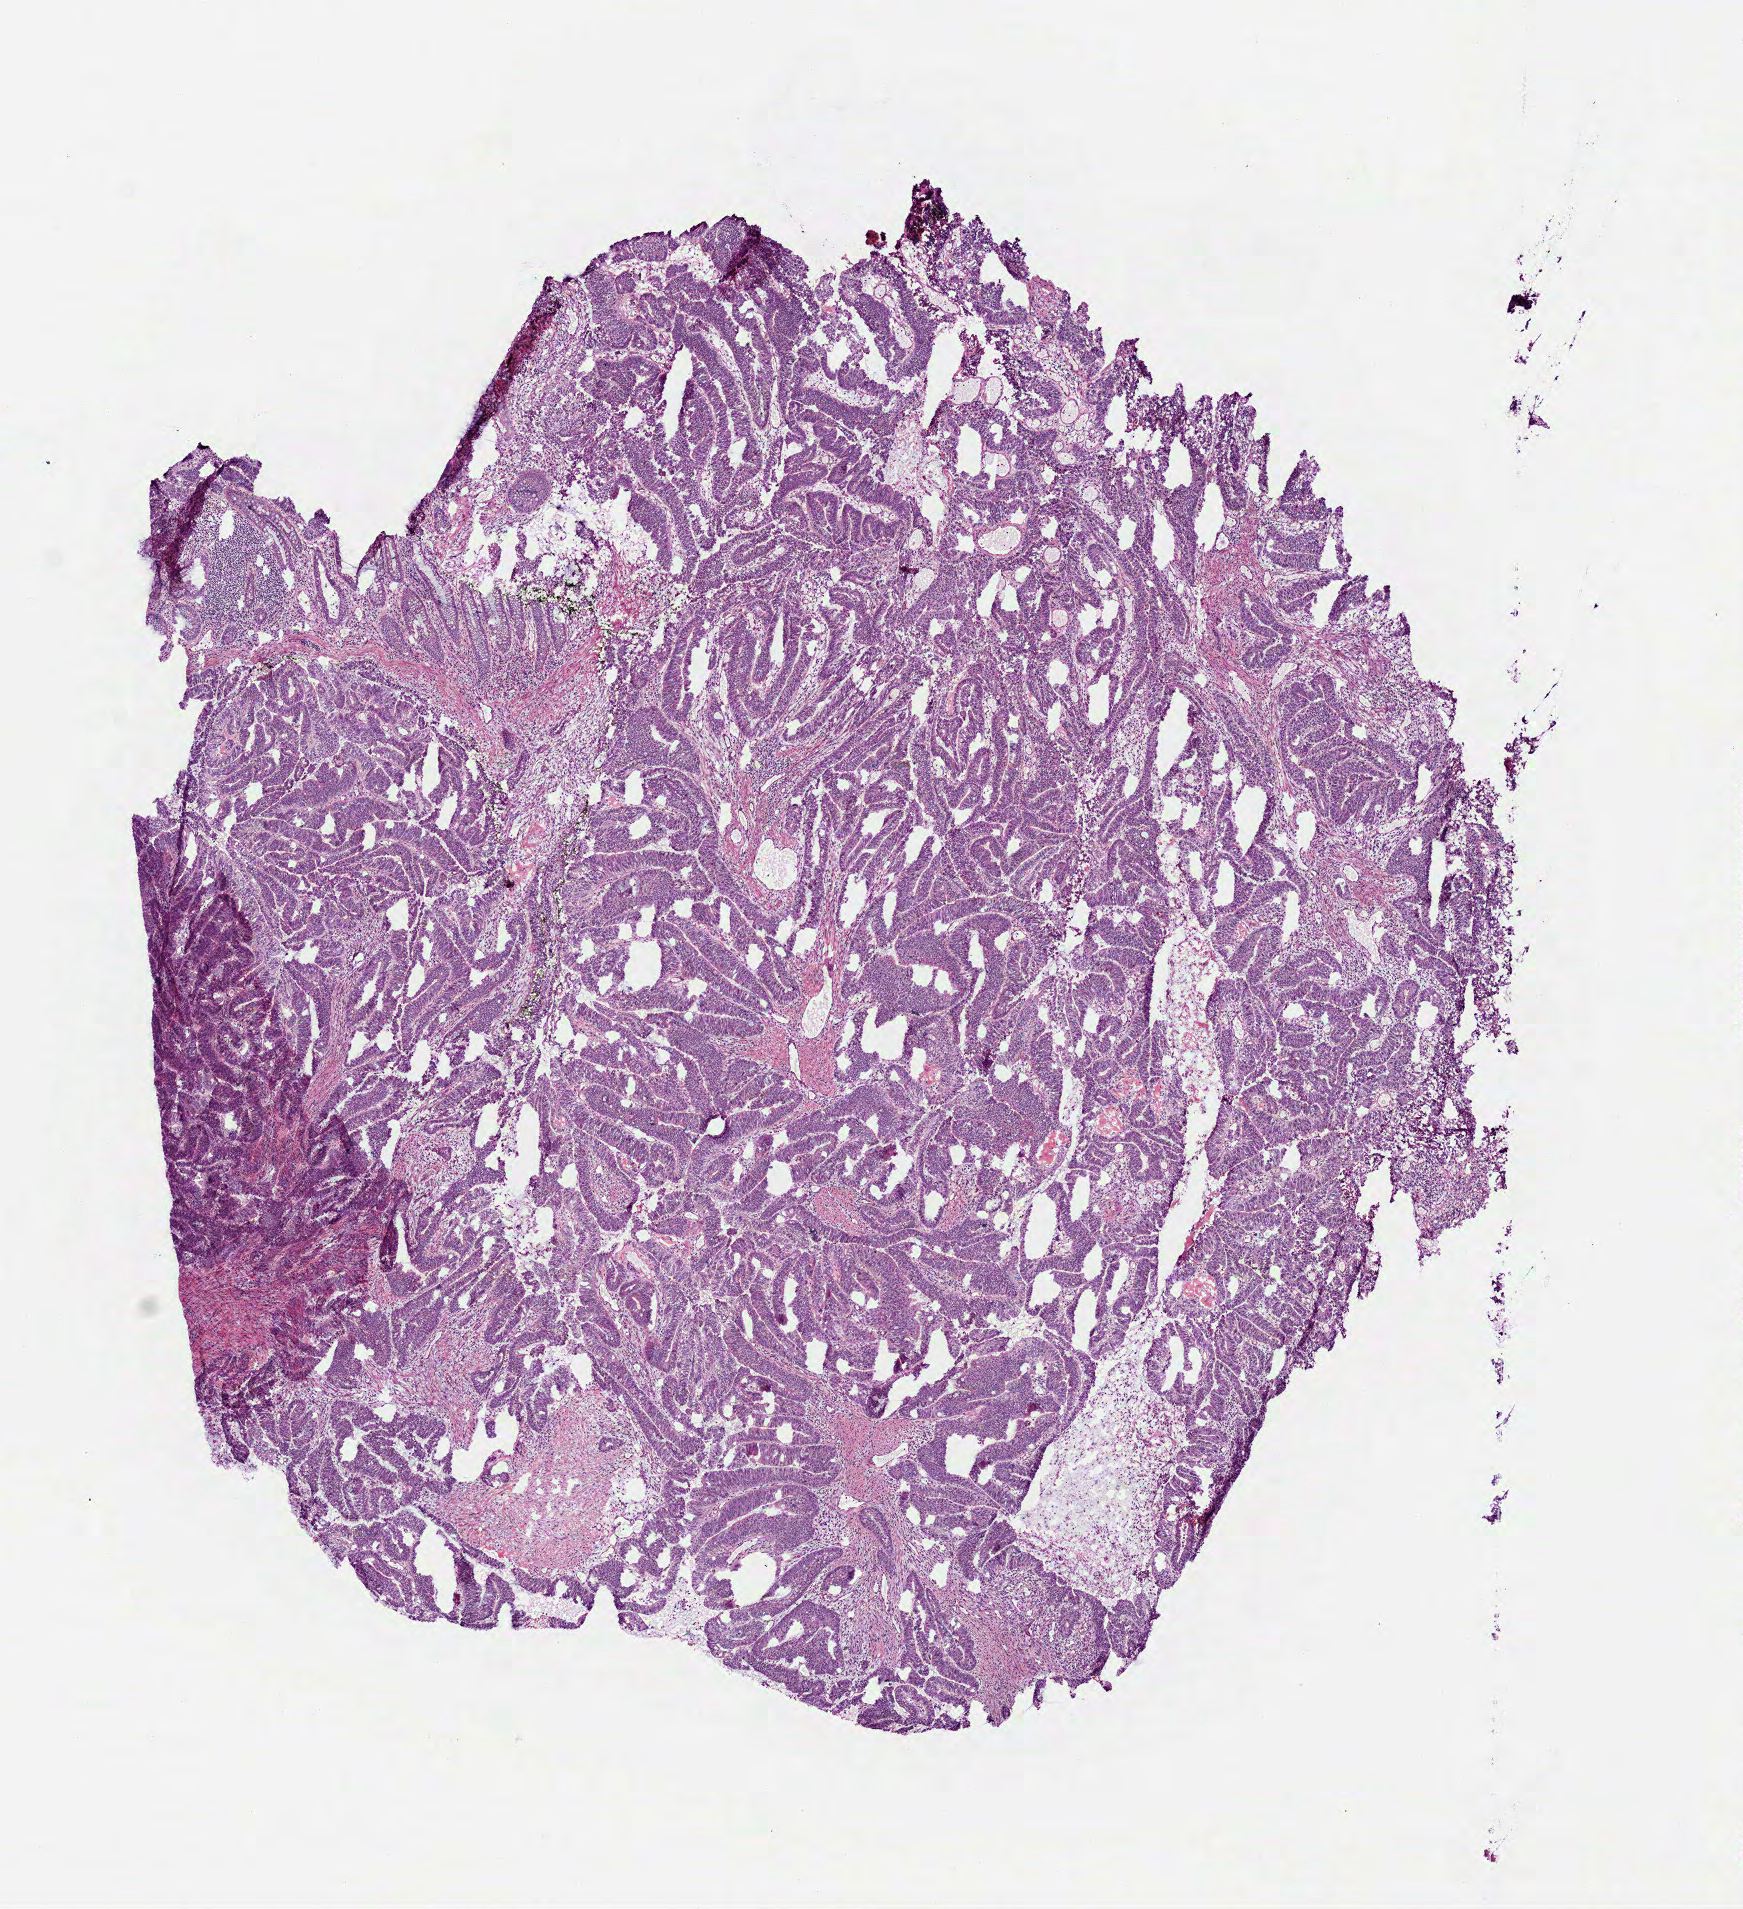
Whole-slide histology image, Hematoxylin and eosin (H&E) stained — whole scanned area (about 7.0 x 7.7 mm) shown as a low-resolution overview, frozen section, sample: primary tumour, rectum. Male patient; age at initial diagnosis 43 years.
Diagnosis: Adenocarcinoma, NOS (rectosigmoid junction).